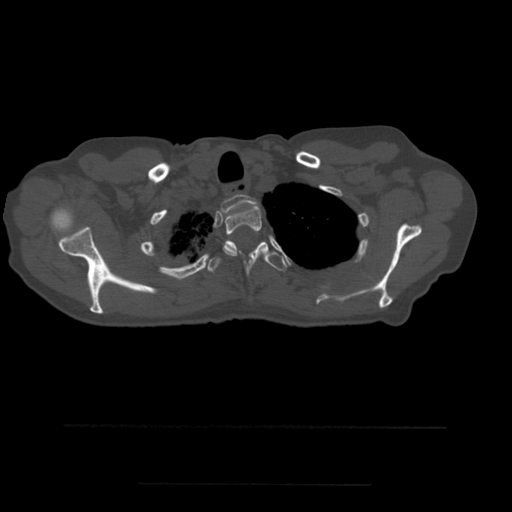
CT including the spine, one axial slice; slice 430 of 544 in the series (ordered by position); bone window (W 1800 / L 400 HU); 512 × 512 image matrix, field of view 350 × 350 mm. Patient age 58 years. Case-level facts recorded for this patient, not image findings: primary cancer: lung.
Structures marked on this image (semi-automatic segmentation, software-assisted and operator-edited):
- T1 vertebra: bounding box [x1, y1, x2, y2] px = [221, 194, 258, 213]
- T2 vertebra: [223, 205, 262, 257]
- T3 vertebra: [208, 241, 288, 275]